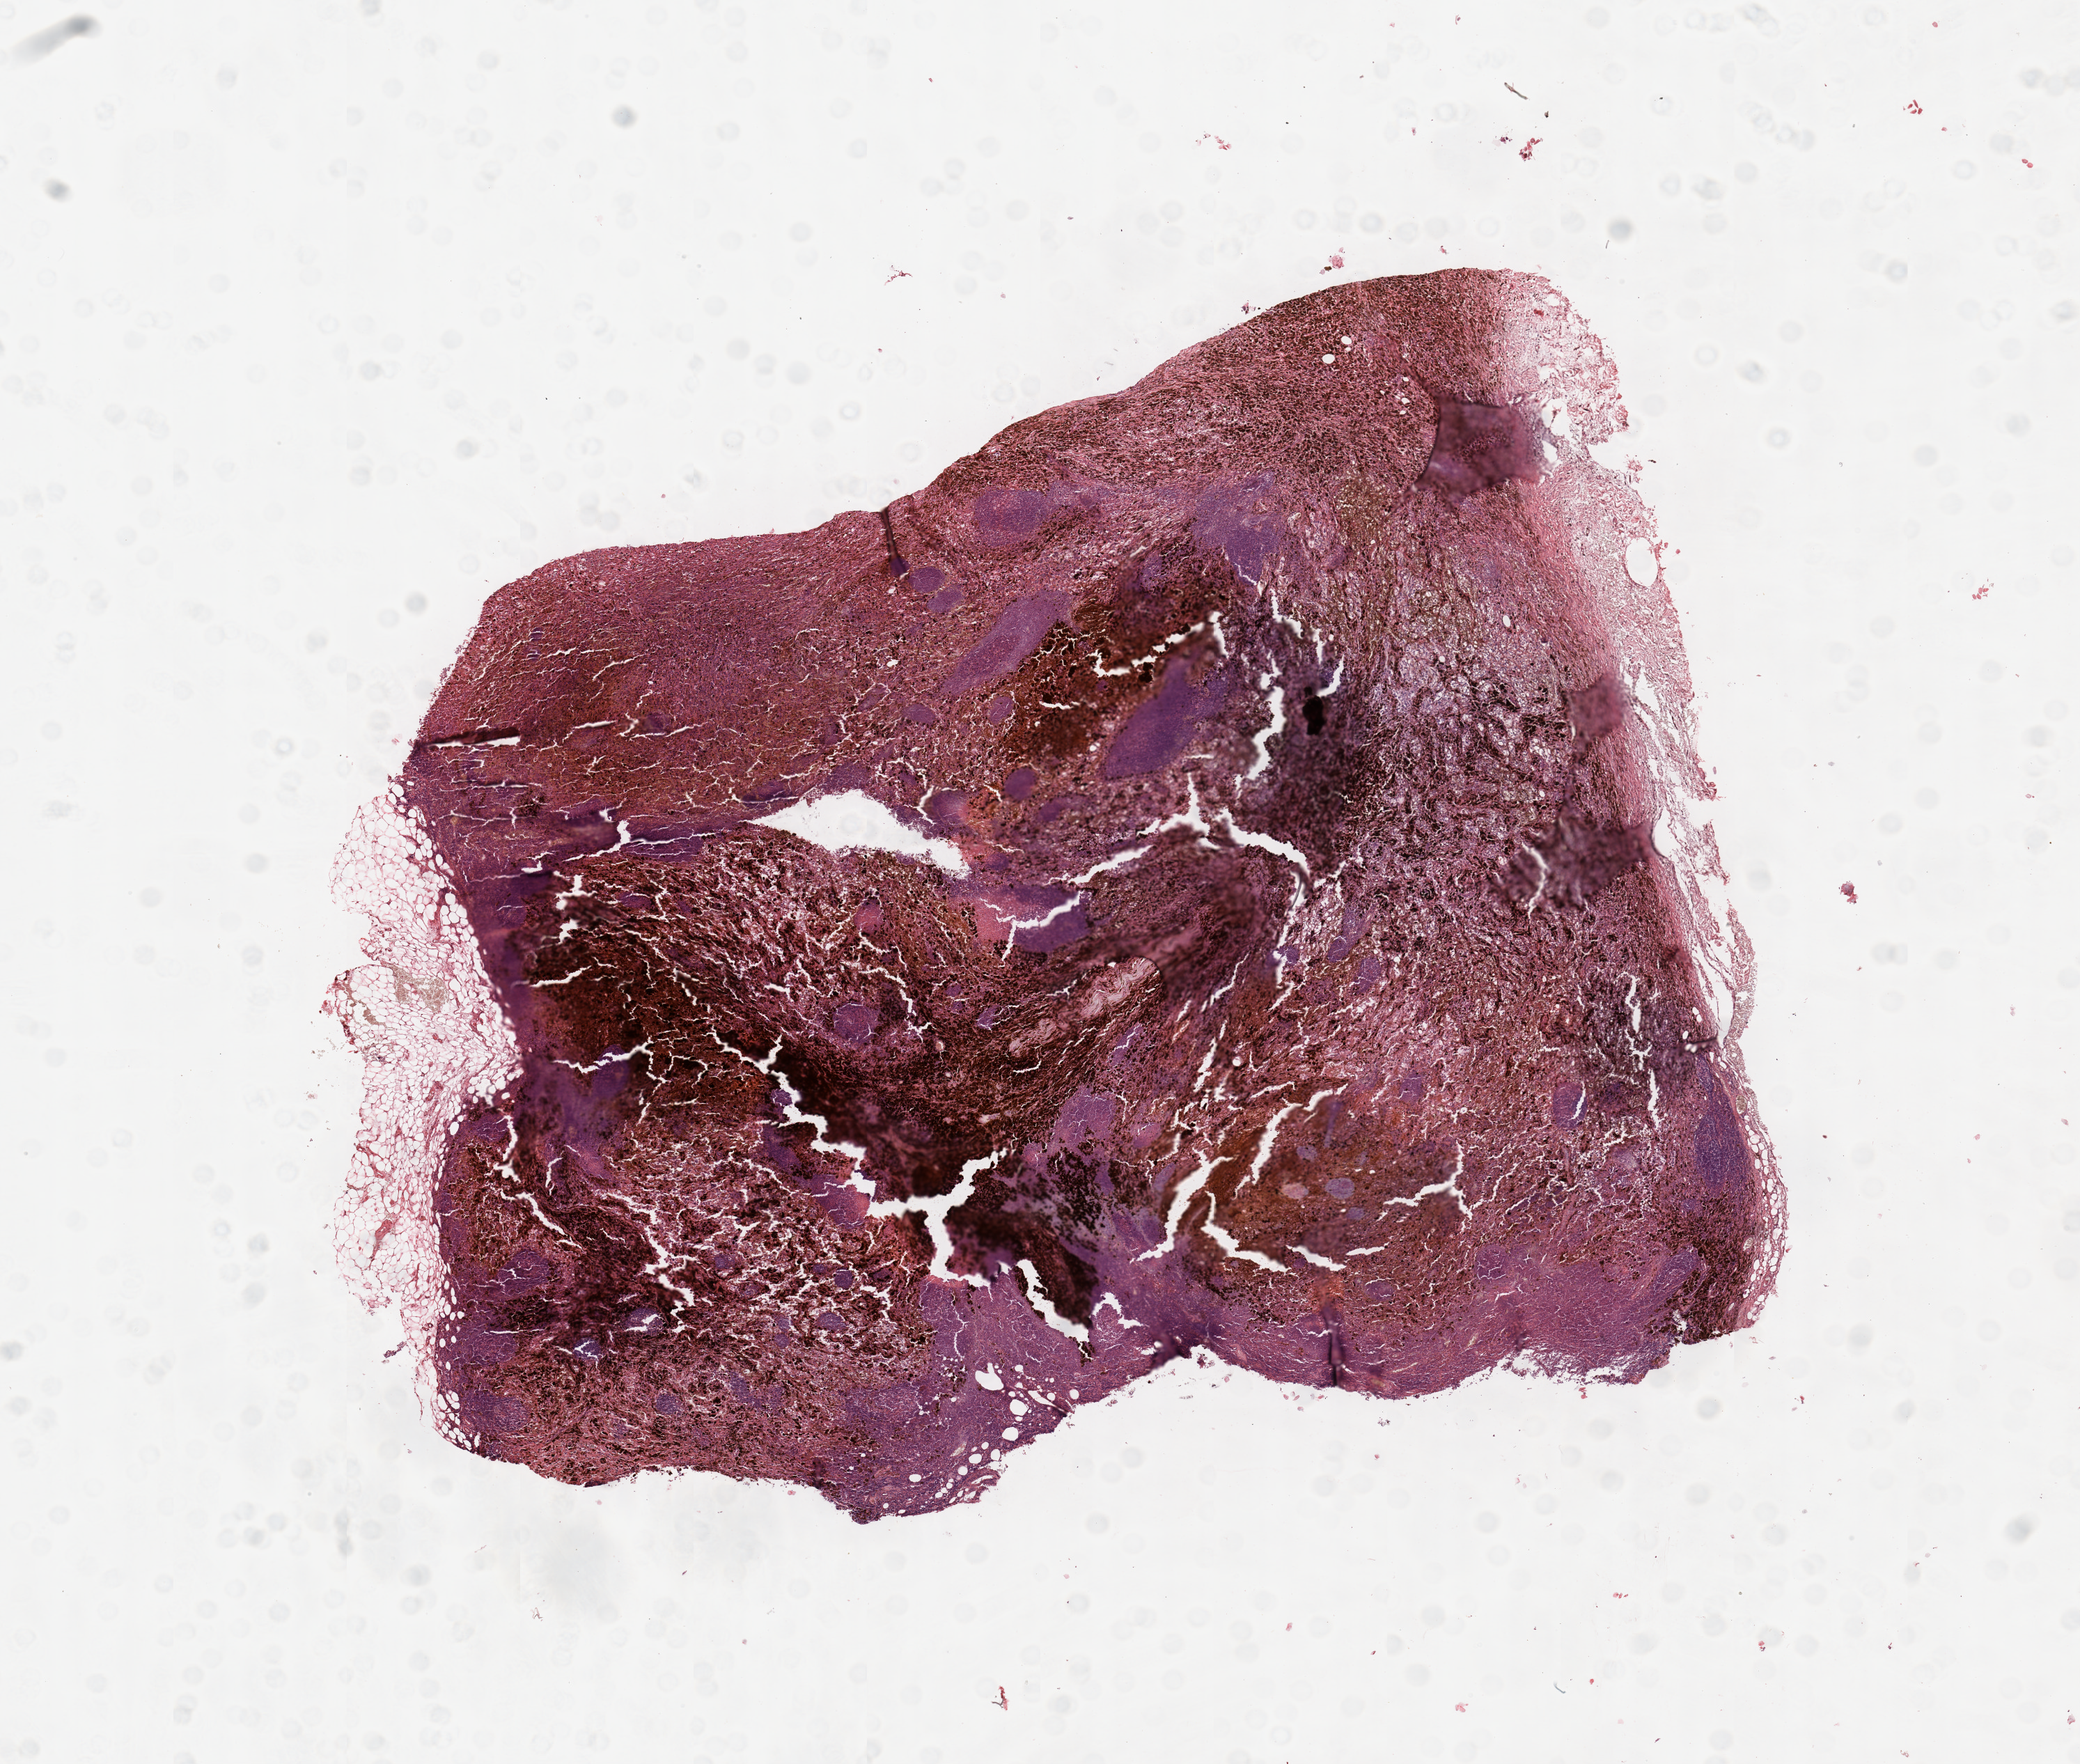
Digitized Hematoxylin and eosin (H&E) stained tissue section (whole slide) — whole scanned area (about 11.8 x 10.0 mm) shown as a low-resolution overview, melanoma tumour tissue; sampled site not recorded. Male, 74 y/o.
Patient diagnosis (cohort enrolment): cutaneous melanoma (skin).